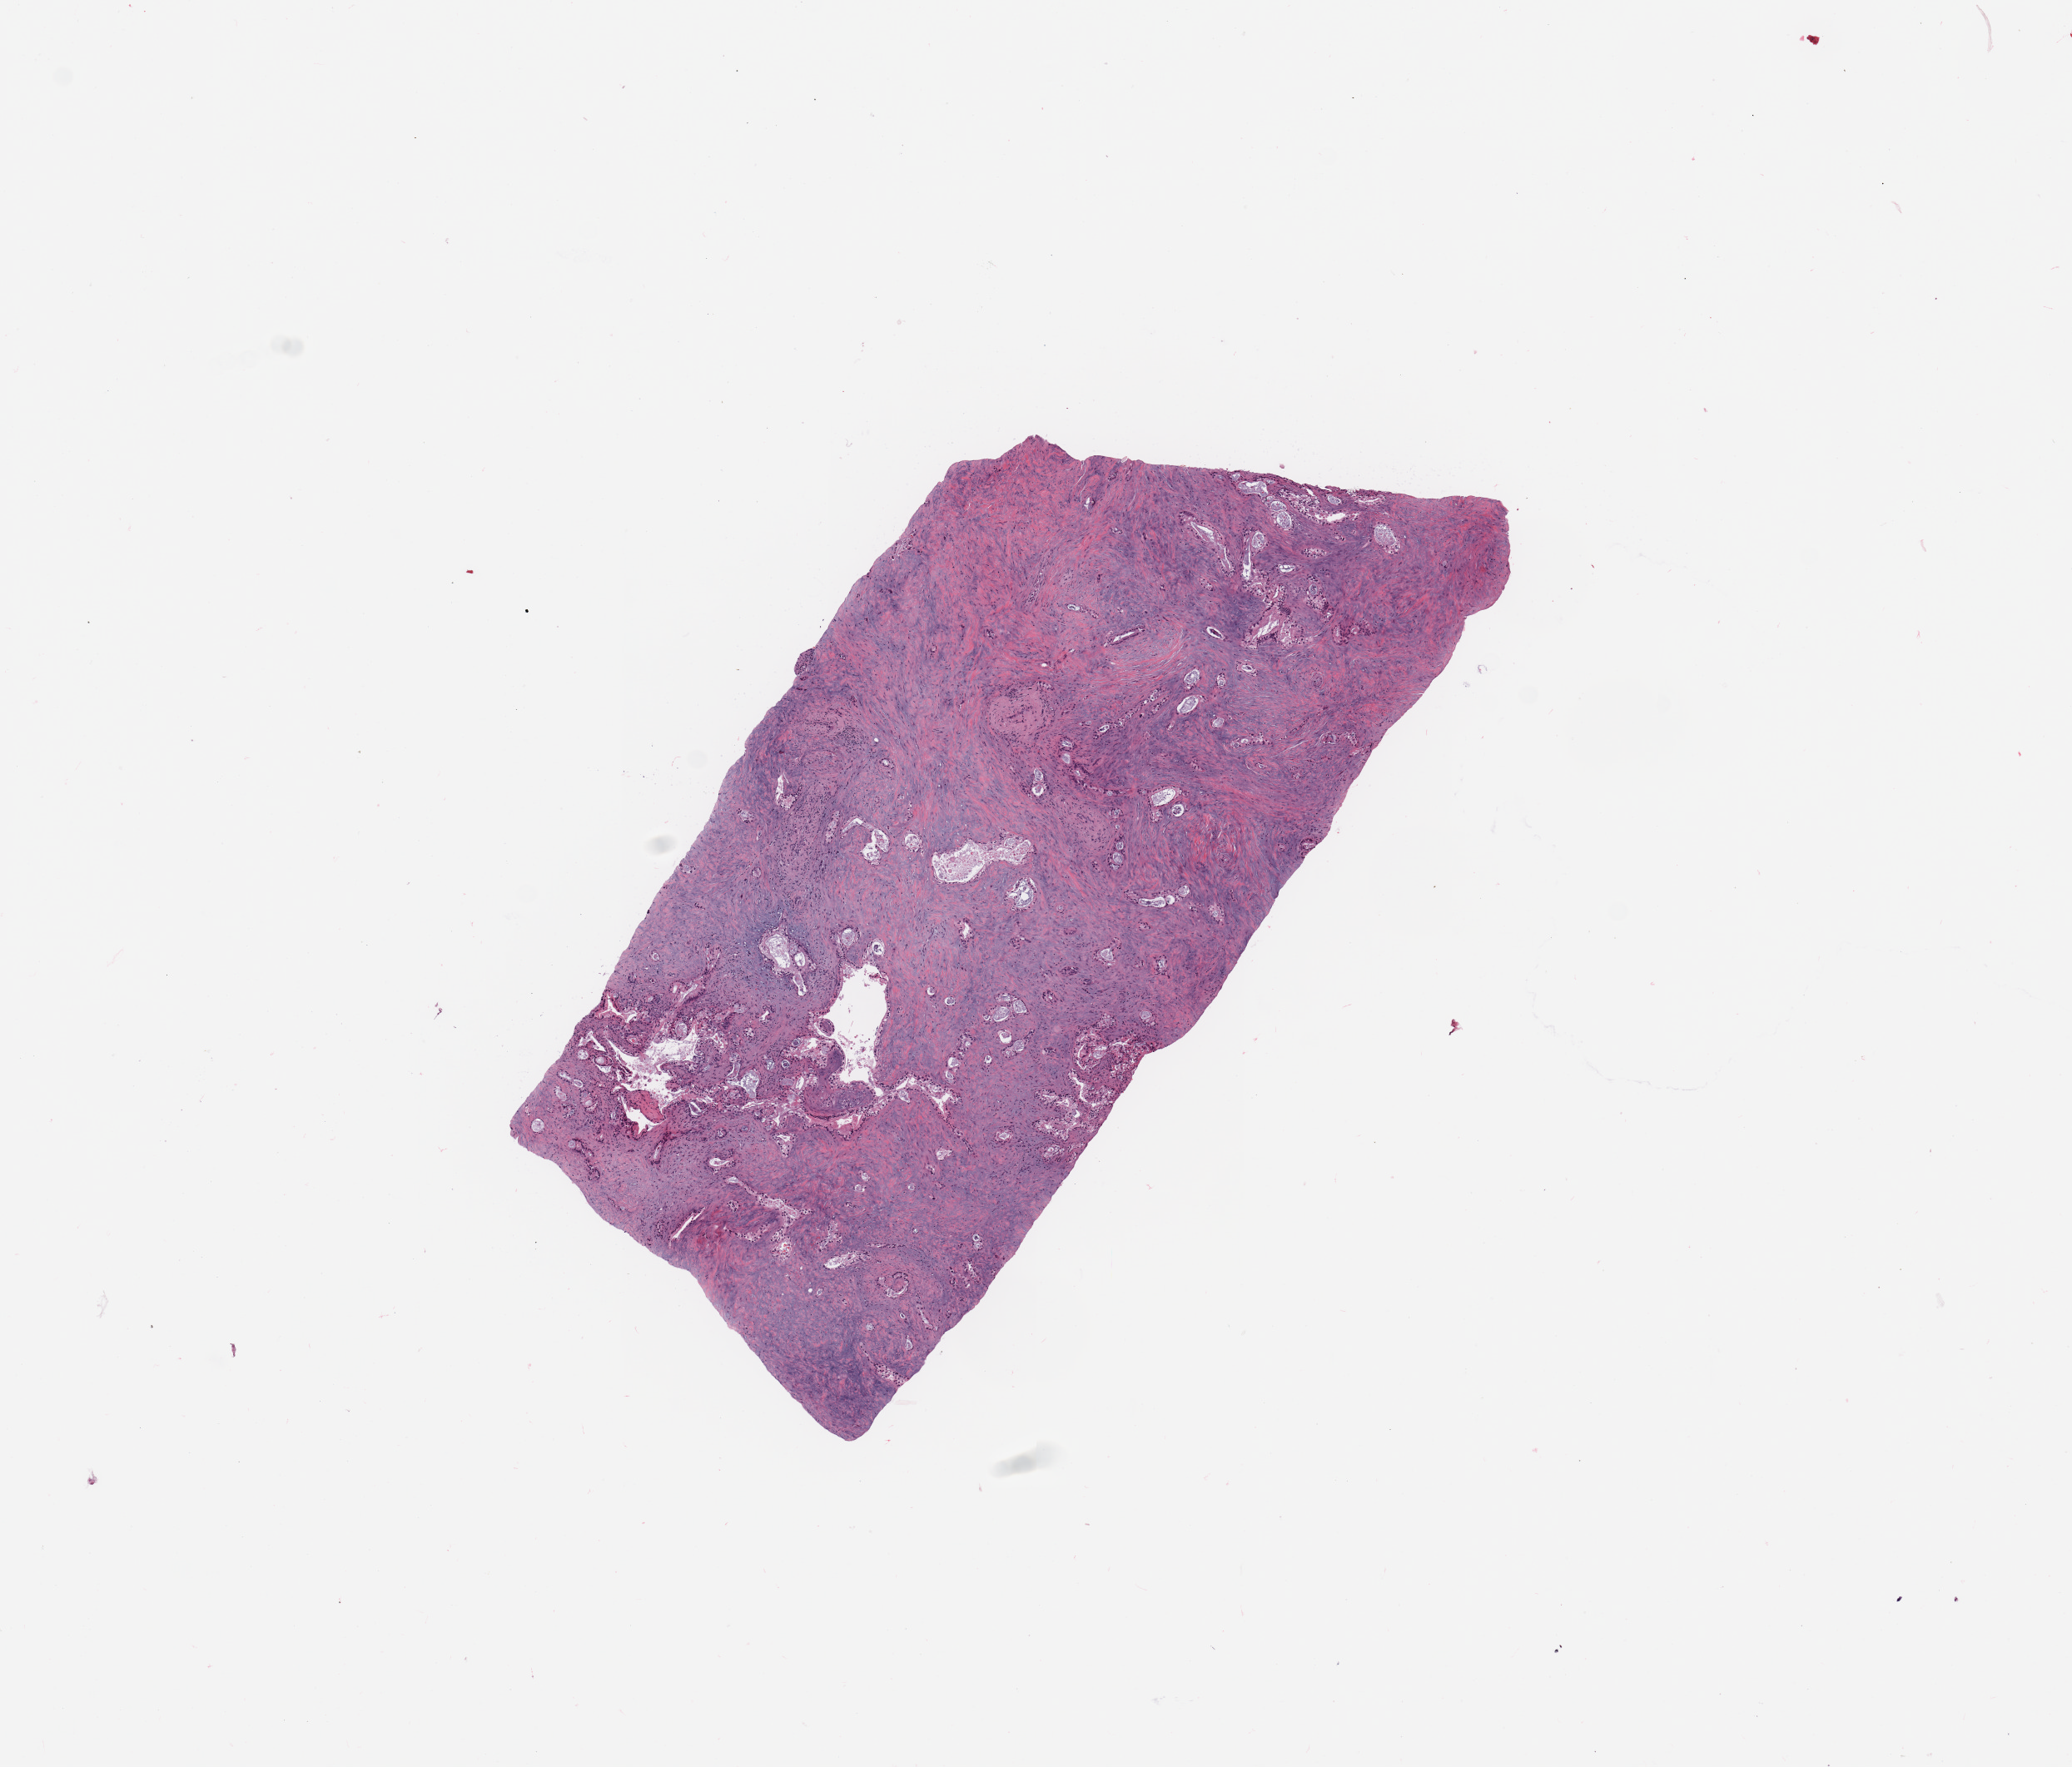
Whole-slide histology image, H&E-stained, low-resolution overview of the scanned area, about 9.8 x 8.4 mm (from a 20x scan). Pancreas, tumour tissue. 84-year-old male patient. Histologic grade: G2 (moderately differentiated).
Diagnosis: Infiltrating duct carcinoma, NOS. Primary tumour site (as recorded): head. AJCC pathologic stage: III.